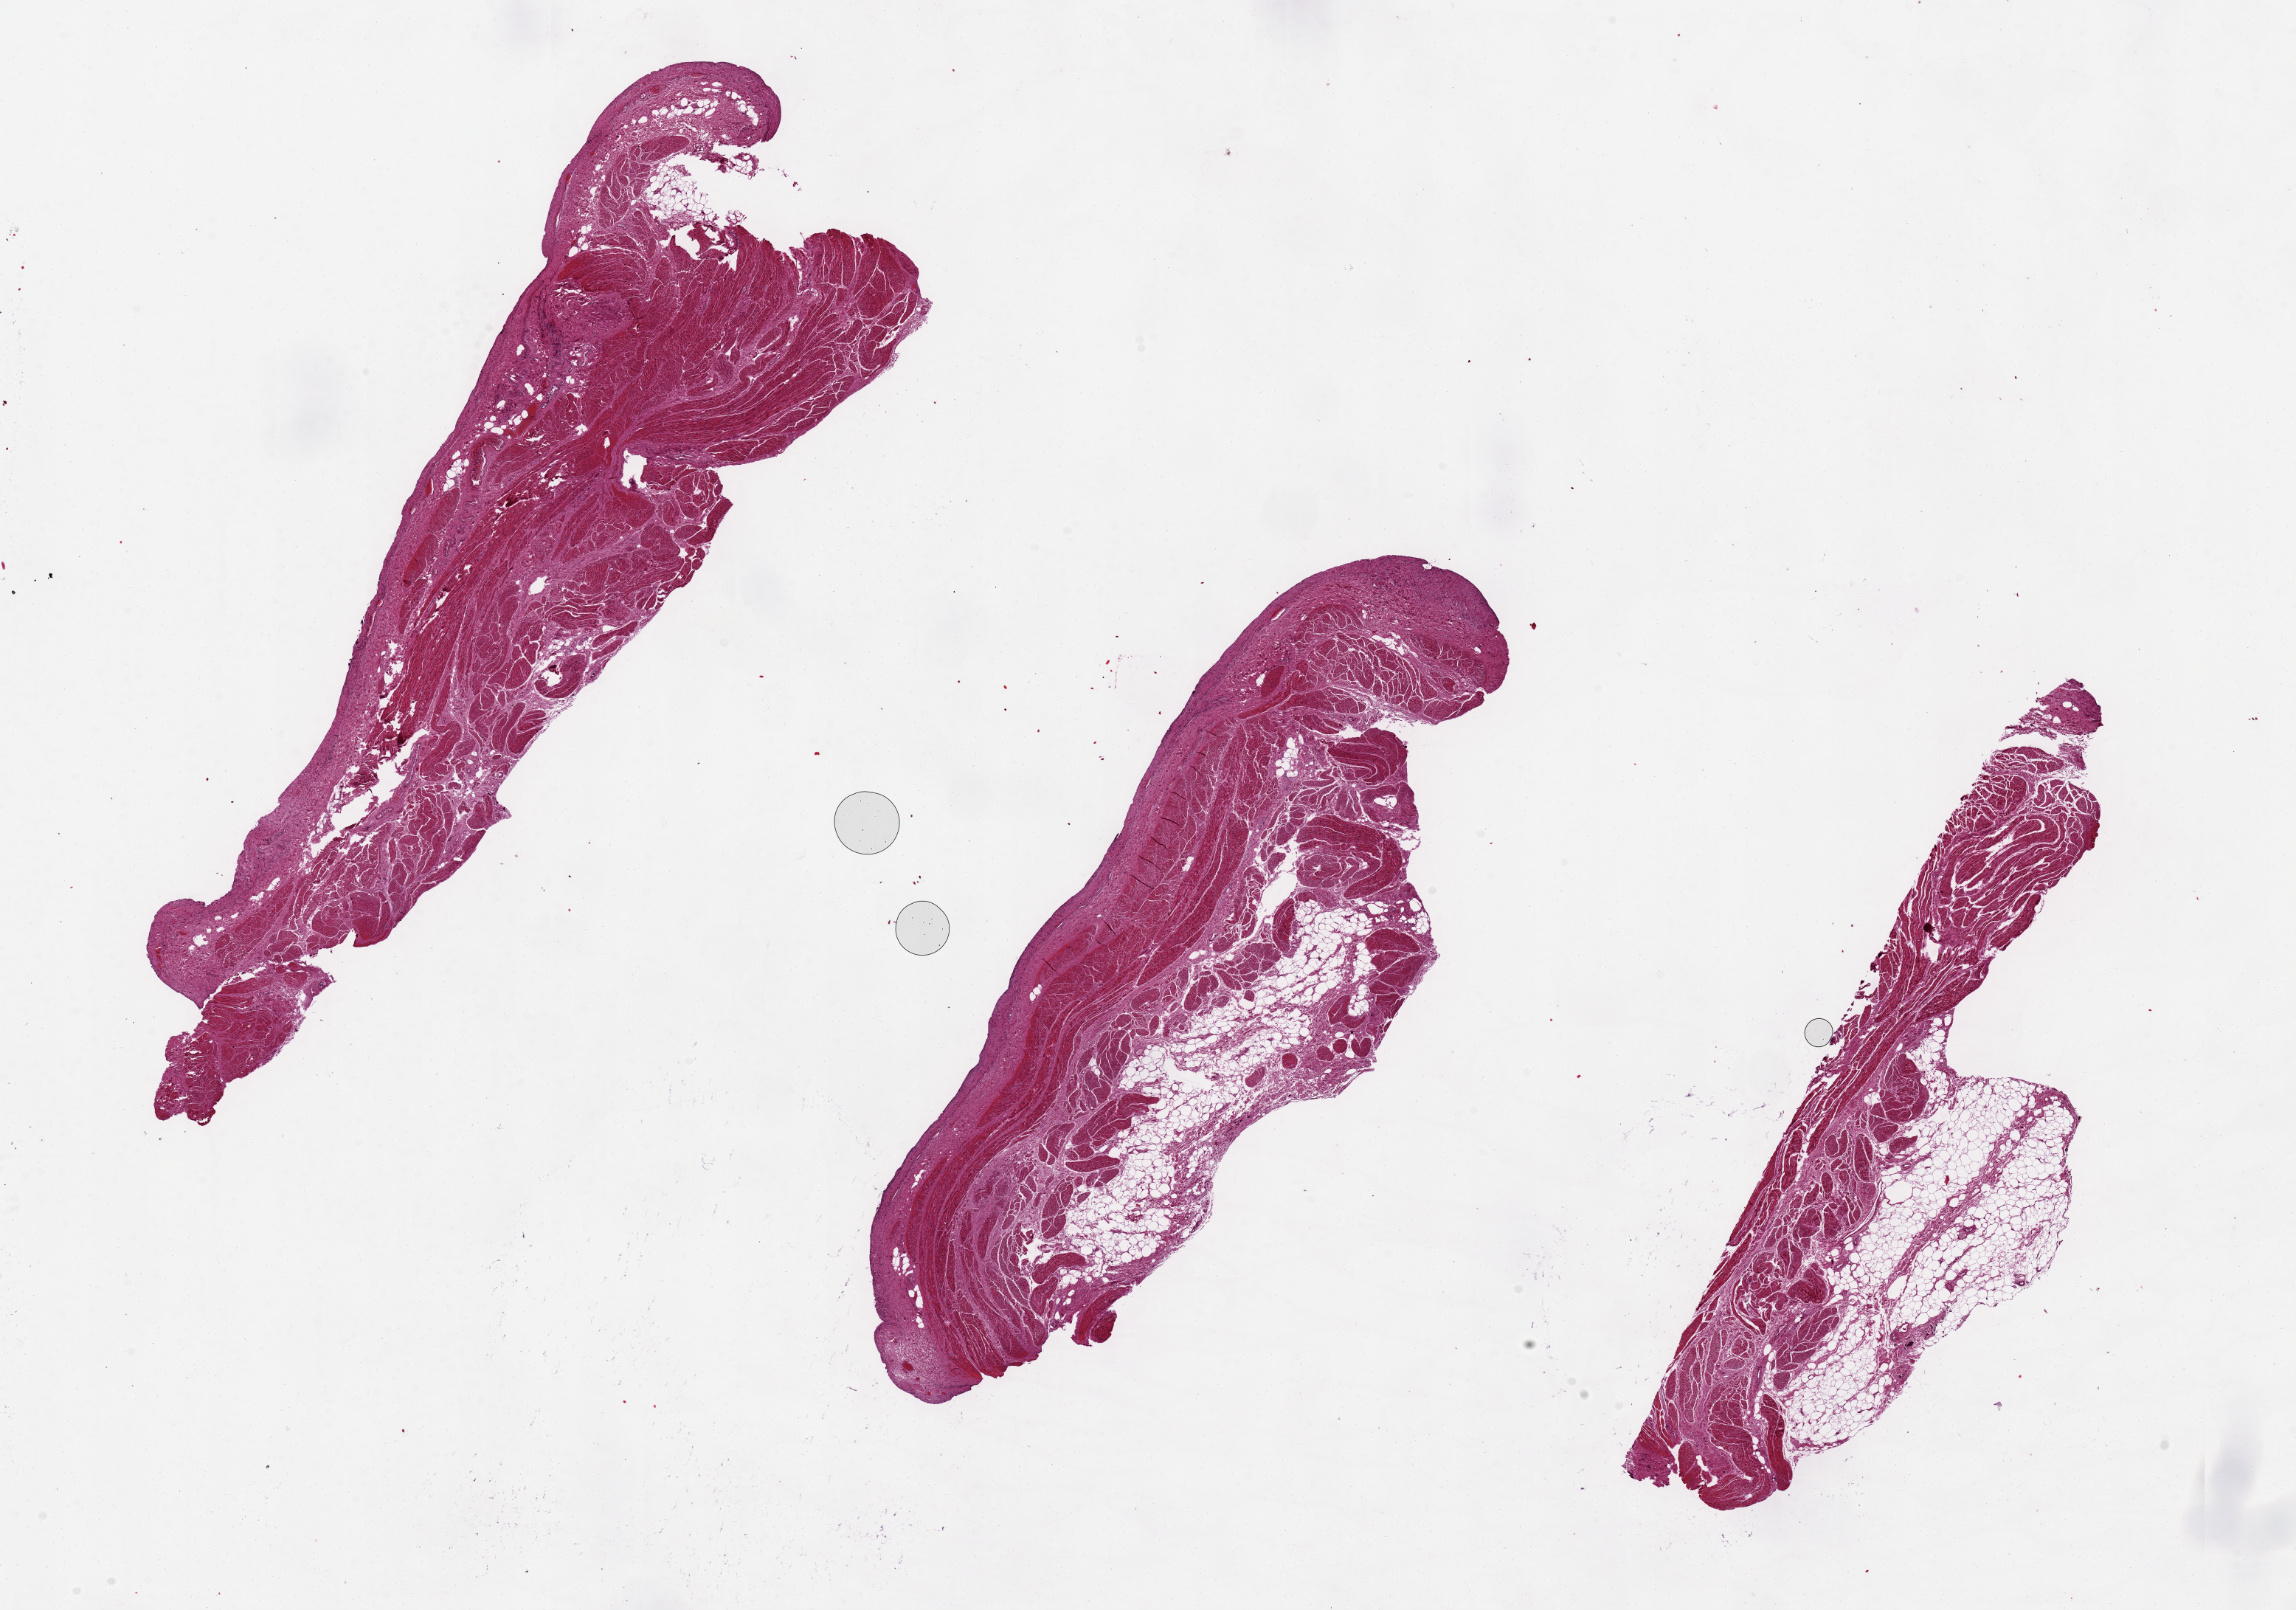
Whole-slide image, hematoxylin and eosin (H&E) stain, low-resolution overview of the scanned area, about 24.6 x 17.3 mm; PAXgene-fixed, paraffin-embedded tissue; sampled site (target tissue): urinary bladder; donor tissue sample. Donor sex: male.
Pathologist's review note for this sample: Completely sloughed epithelium; preserved muscle.